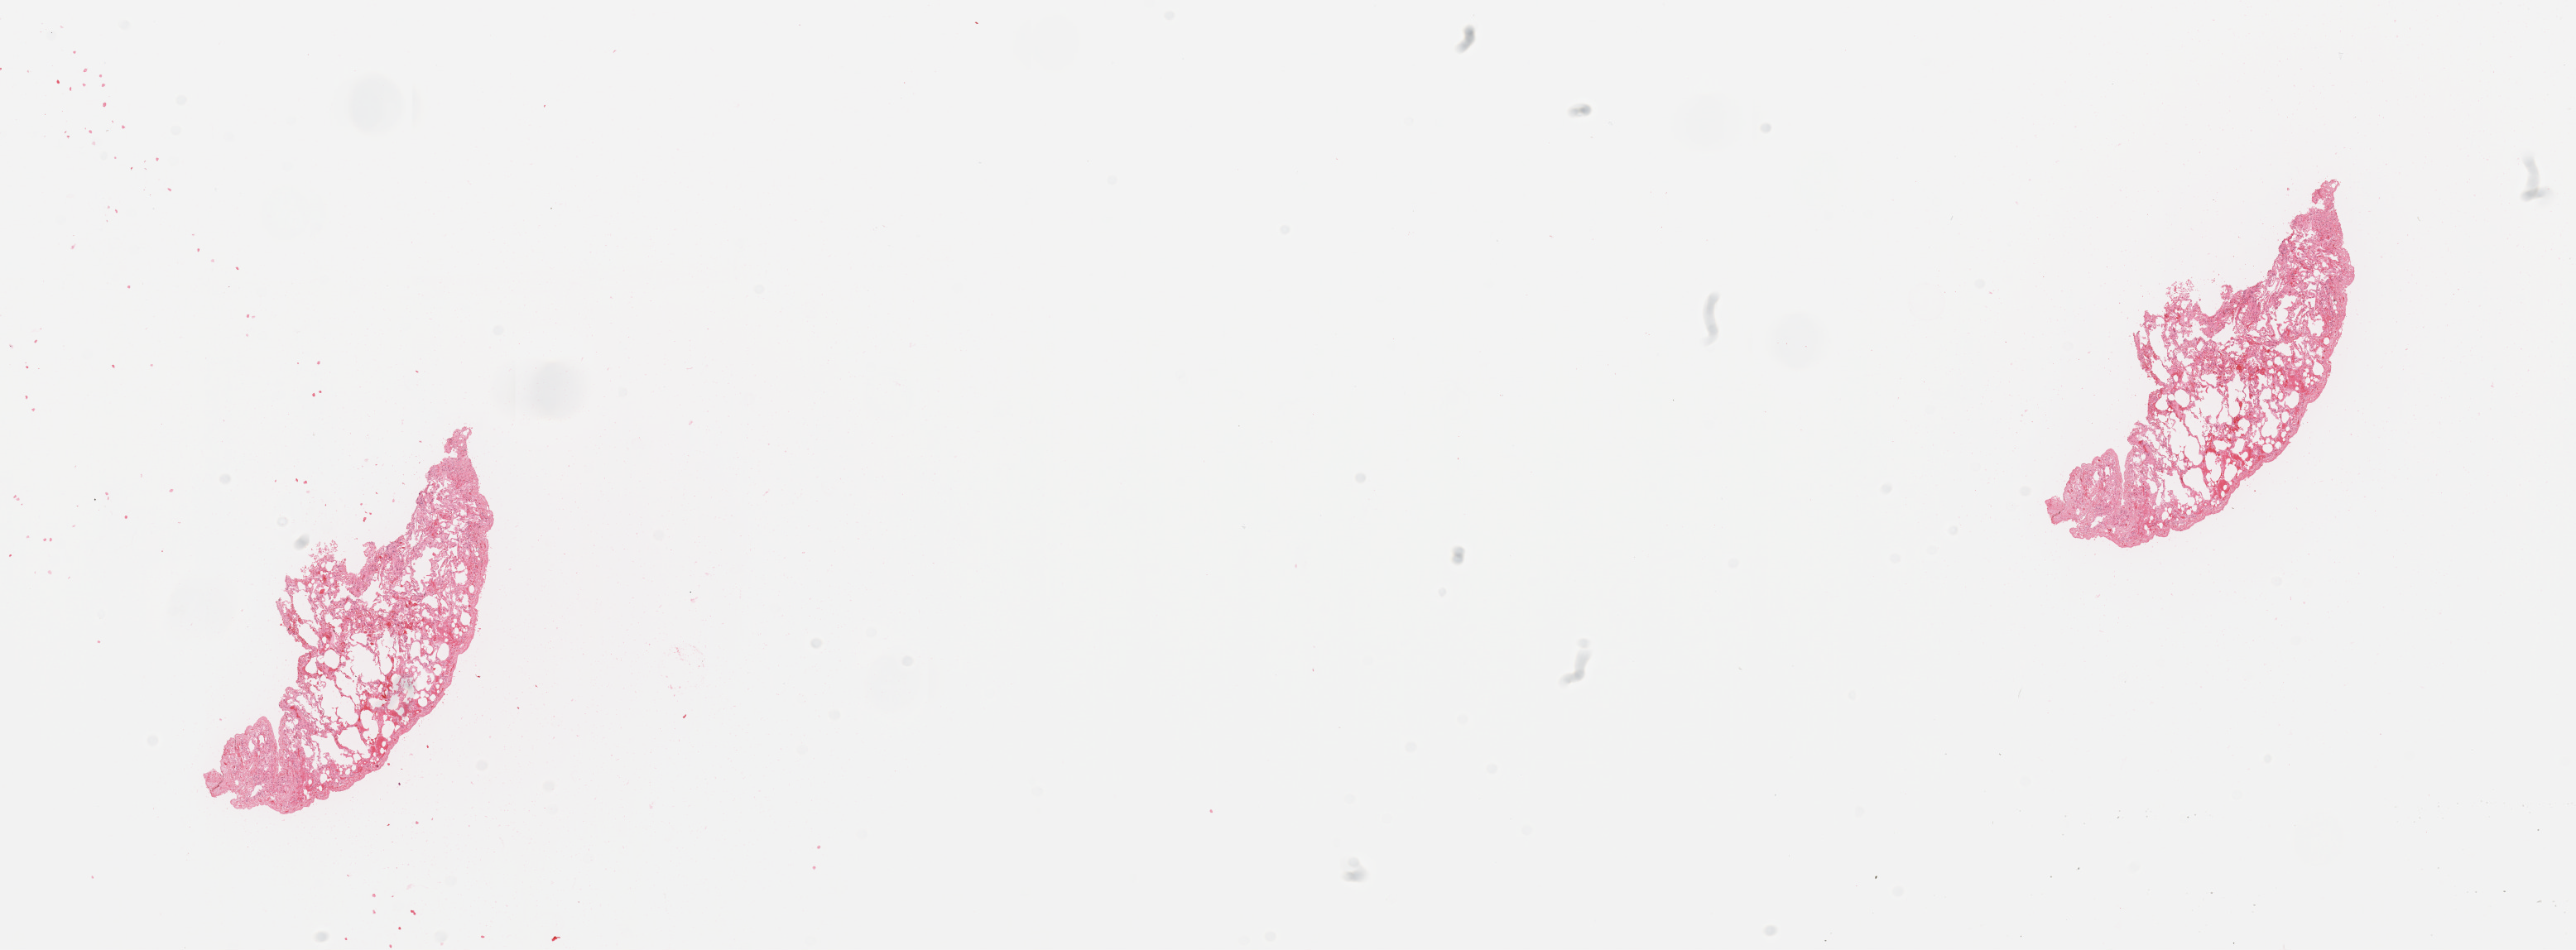
Whole-slide histology image, H&E-stained, shown as a low-resolution overview of the whole scanned area (about 24.6 x 9.1 mm, slide scanned at 20x). Normal (non-tumour) tissue sample, sampled site: lung. Patient: female, age 72 years.
This section: normal (non-tumour) tissue from the same patient. Patient diagnosis: Adenocarcinoma, NOS.